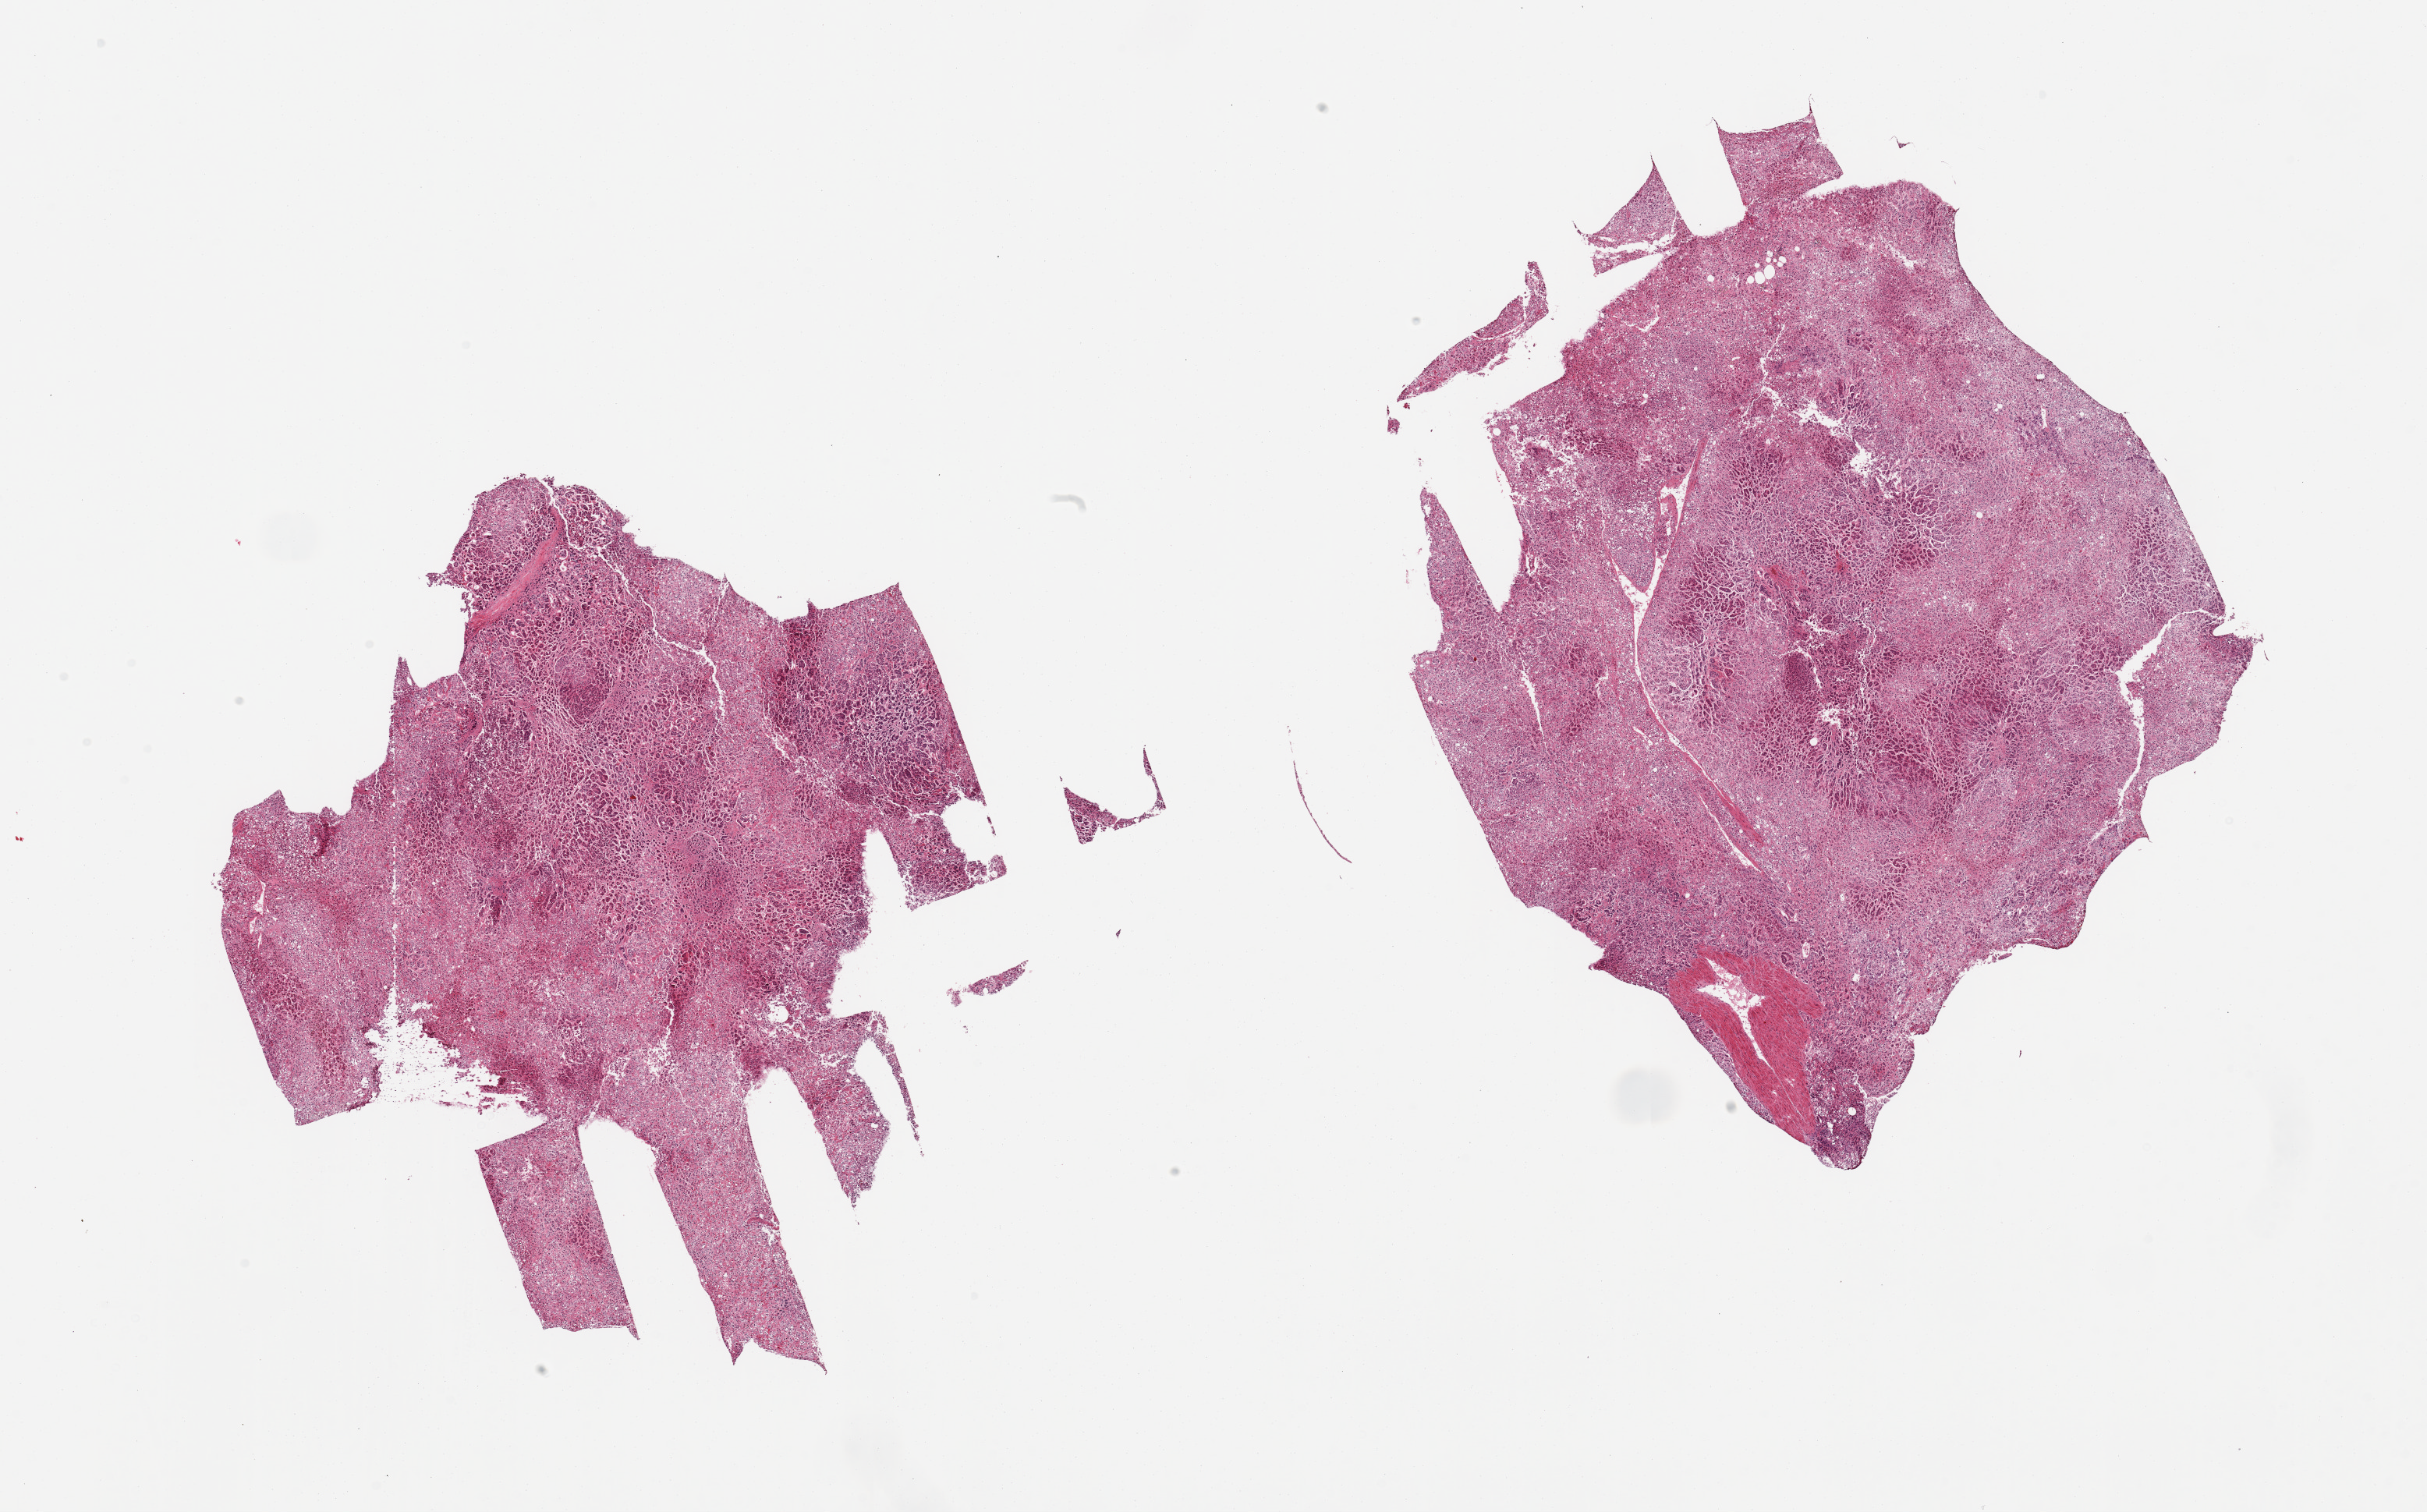
Whole-slide image, hematoxylin and eosin (H&E) stain, shown as a low-resolution overview of the whole scanned area (about 24.6 x 15.3 mm), PAXgene-fixed, paraffin-embedded tissue, sampled site (target tissue): adrenal gland, donor tissue sample.
Pathologist's review note for this sample: 2 pieces, all cortex.